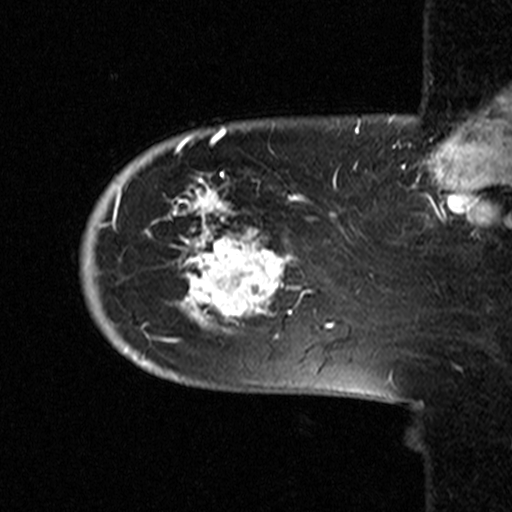
Breast MRI (dynamic contrast-enhanced), one sagittal slice. Slice 9 of 44 in the series (ordered by position). Dynamic contrast-enhanced study with each time point stored as its own series, time point 2 of 3 at this slice position (early post-contrast, ordered by acquisition time). 1.5 T. TE 4.5 ms, TR 11 ms. 3.27 mm slice thickness. 512 × 512 image matrix, field of view 200 × 200 mm. Female patient, age 53 years. Case-level facts recorded for this patient, not image findings: setting: breast cancer imaged before/during neoadjuvant chemotherapy; receptor status: HR-positive, HER2-negative.
Annotated regions visible in this slice (semi-automatically segmented with operator editing):
- analysis volume of interest (the breast-tissue region the enhancement analysis was run in; not a lesion): bounding box <75,154,311,367> (left, top, right, bottom; pixels)
- tumour enhancement mask (voxels above the 90 % enhancement threshold inside the analysis volume of interest): <113,170,311,342>